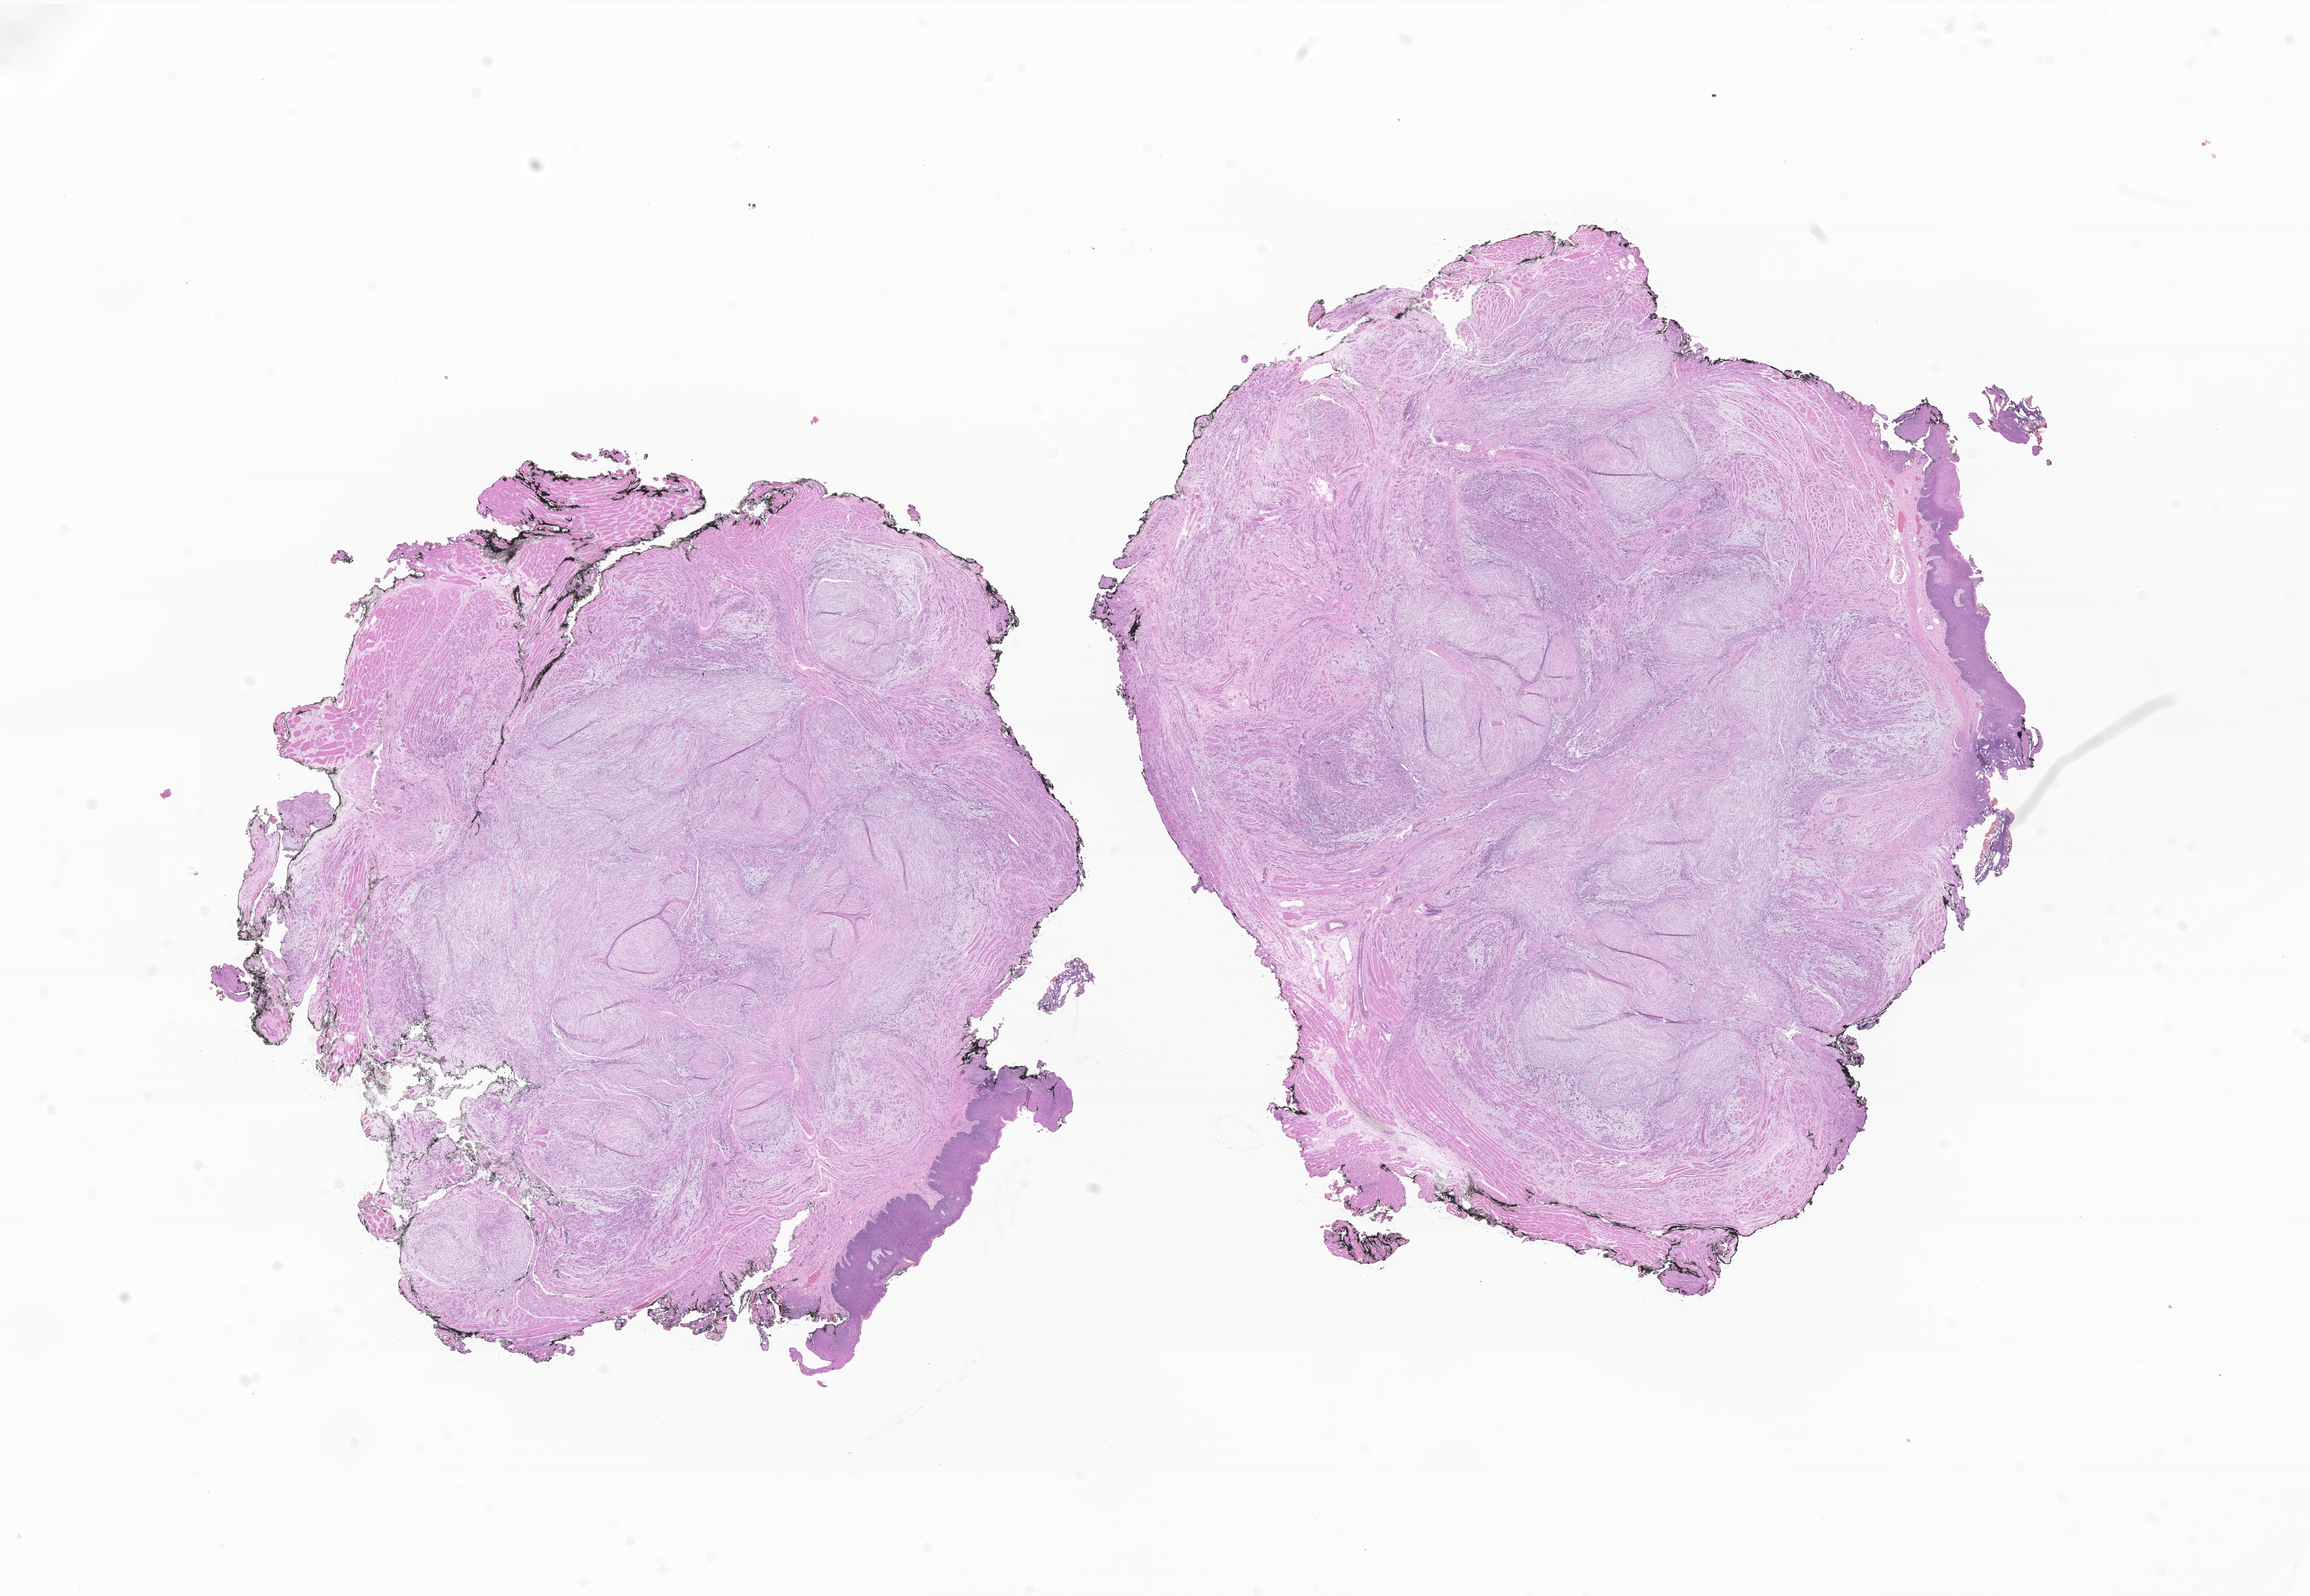
Haematoxylin and eosin whole-slide image of tumor tissue from the tongue — shown as a low-resolution overview of the whole scanned area (about 19.9 x 13.7 mm); formalin-fixed paraffin-embedded section. Female patient, age 440 days (about 1.2 years).
Diagnosis: Spindle cell rhabdomyosarcoma.